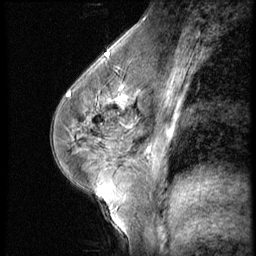
Breast MRI (dynamic contrast-enhanced), one sagittal slice. Slice 30 of 56 in the series (ordered by position). 3 images stored at this slice position (order not interpretable as contrast timing). 1.5 T. TE 4.2 ms, TR 9 ms. 2.5 mm slice thickness. 256 × 256 image matrix. Patient: female, 45 years. Case-level facts recorded for this patient, not image findings: setting: breast cancer imaged before/during neoadjuvant chemotherapy; receptor status: HR-positive, HER2-negative.
Outlined on this slice (semi-automatically segmented with operator editing):
- analysis volume of interest (the breast-tissue region the enhancement analysis was run in; not a lesion): bounding box [x1, y1, x2, y2] px = [102, 77, 166, 129]
- tumour enhancement mask (voxels above the 140 % enhancement threshold inside the analysis volume of interest): [114, 80, 138, 127]